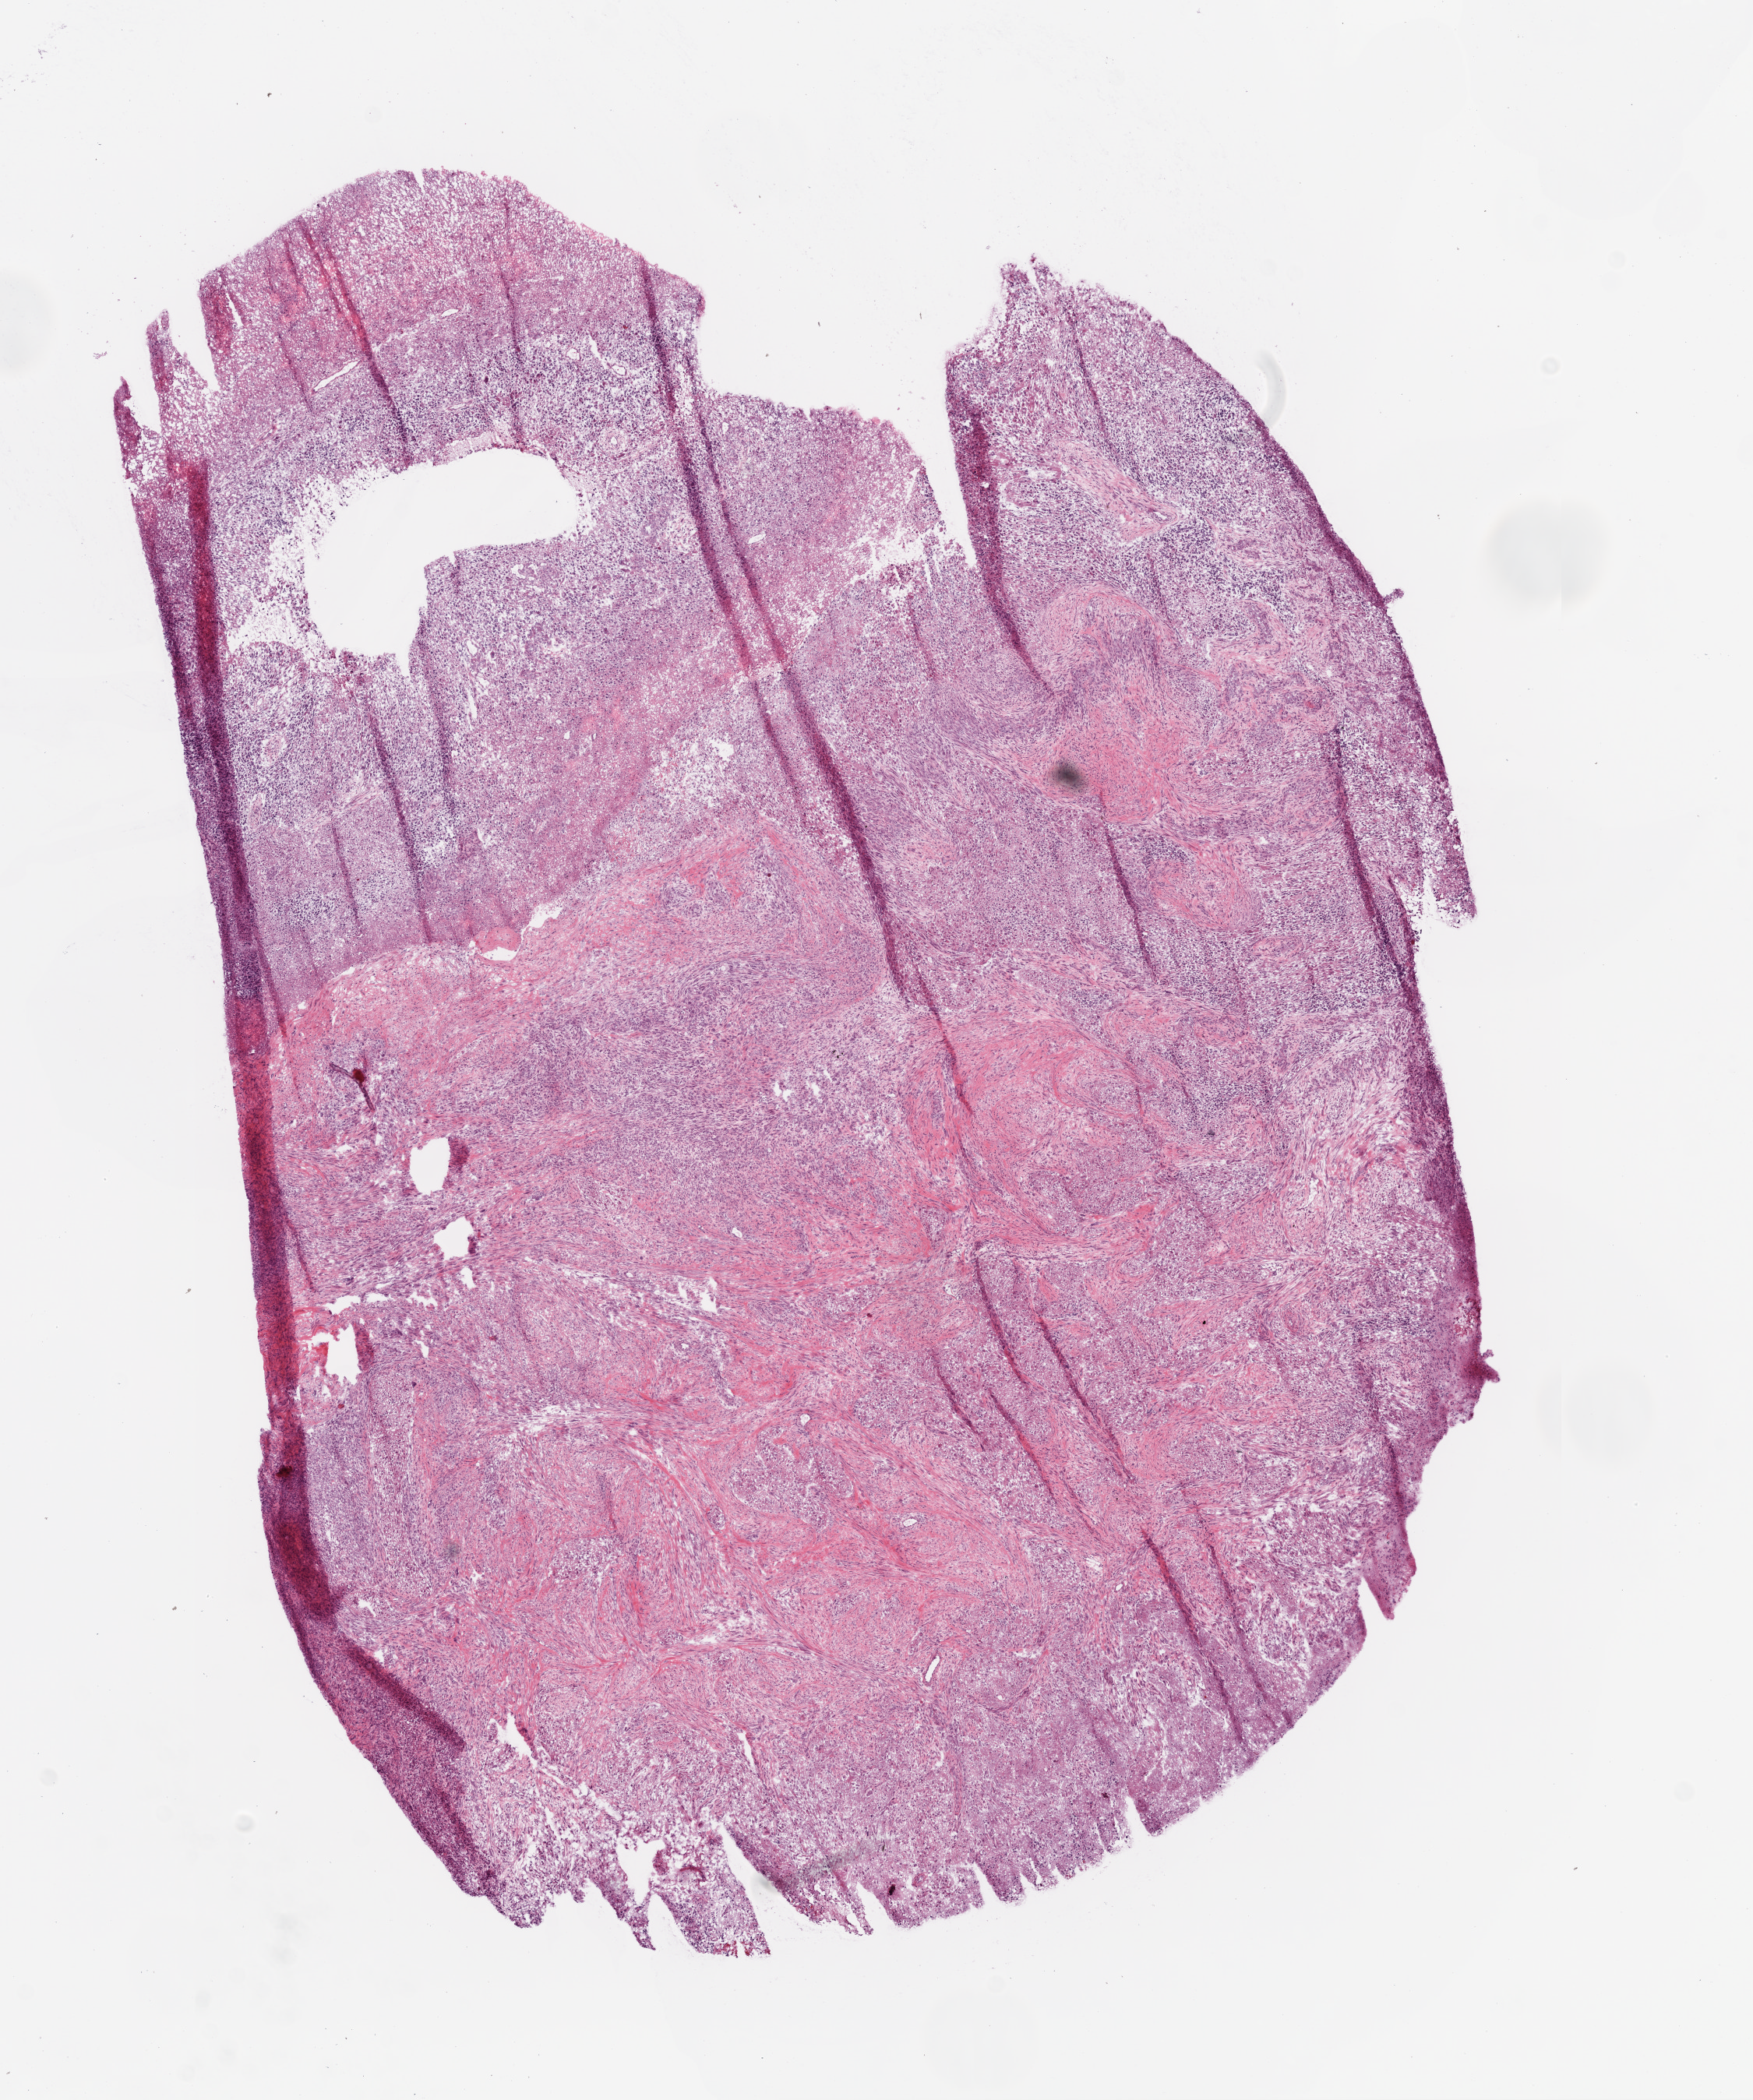
Whole-slide histology image, H&E — whole scanned area (about 9.0 x 10.8 mm) shown as a low-resolution overview, frozen section, brain, primary tumour sample. Male, age 61 years at initial diagnosis. Composition of this section per pathologist review: tumour cells 70%, tumour nuclei 80%, normal cells 5%, stromal cells 20%, necrosis 5%.
Diagnosis: Glioblastoma.